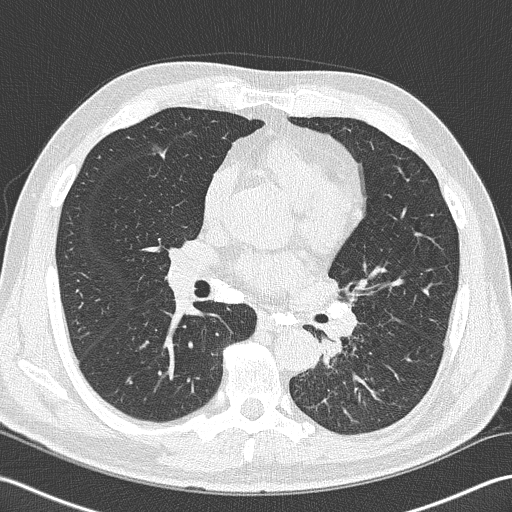
Chest CT (low-dose screening protocol), one axial image. Second annual screen. Lung window (W 1500 / L -600 HU). Lung (sharp) reconstruction kernel (B50f). Male, age 57 years at enrolment.
• Expert reader's lesion annotation, bounding box (x1, y1, x2, y2) in pixels: (293, 298, 372, 380).
• The exam's reader record, not a measurement of the box and not confirmed to be the same lesion: non-calcified nodule or mass ≥4 mm, left lower lobe, 40 × 30 mm, spiculated (stellate) margins, soft tissue attenuation, pre-existing on the prior screen: no.
• Official screen result: positive, other.